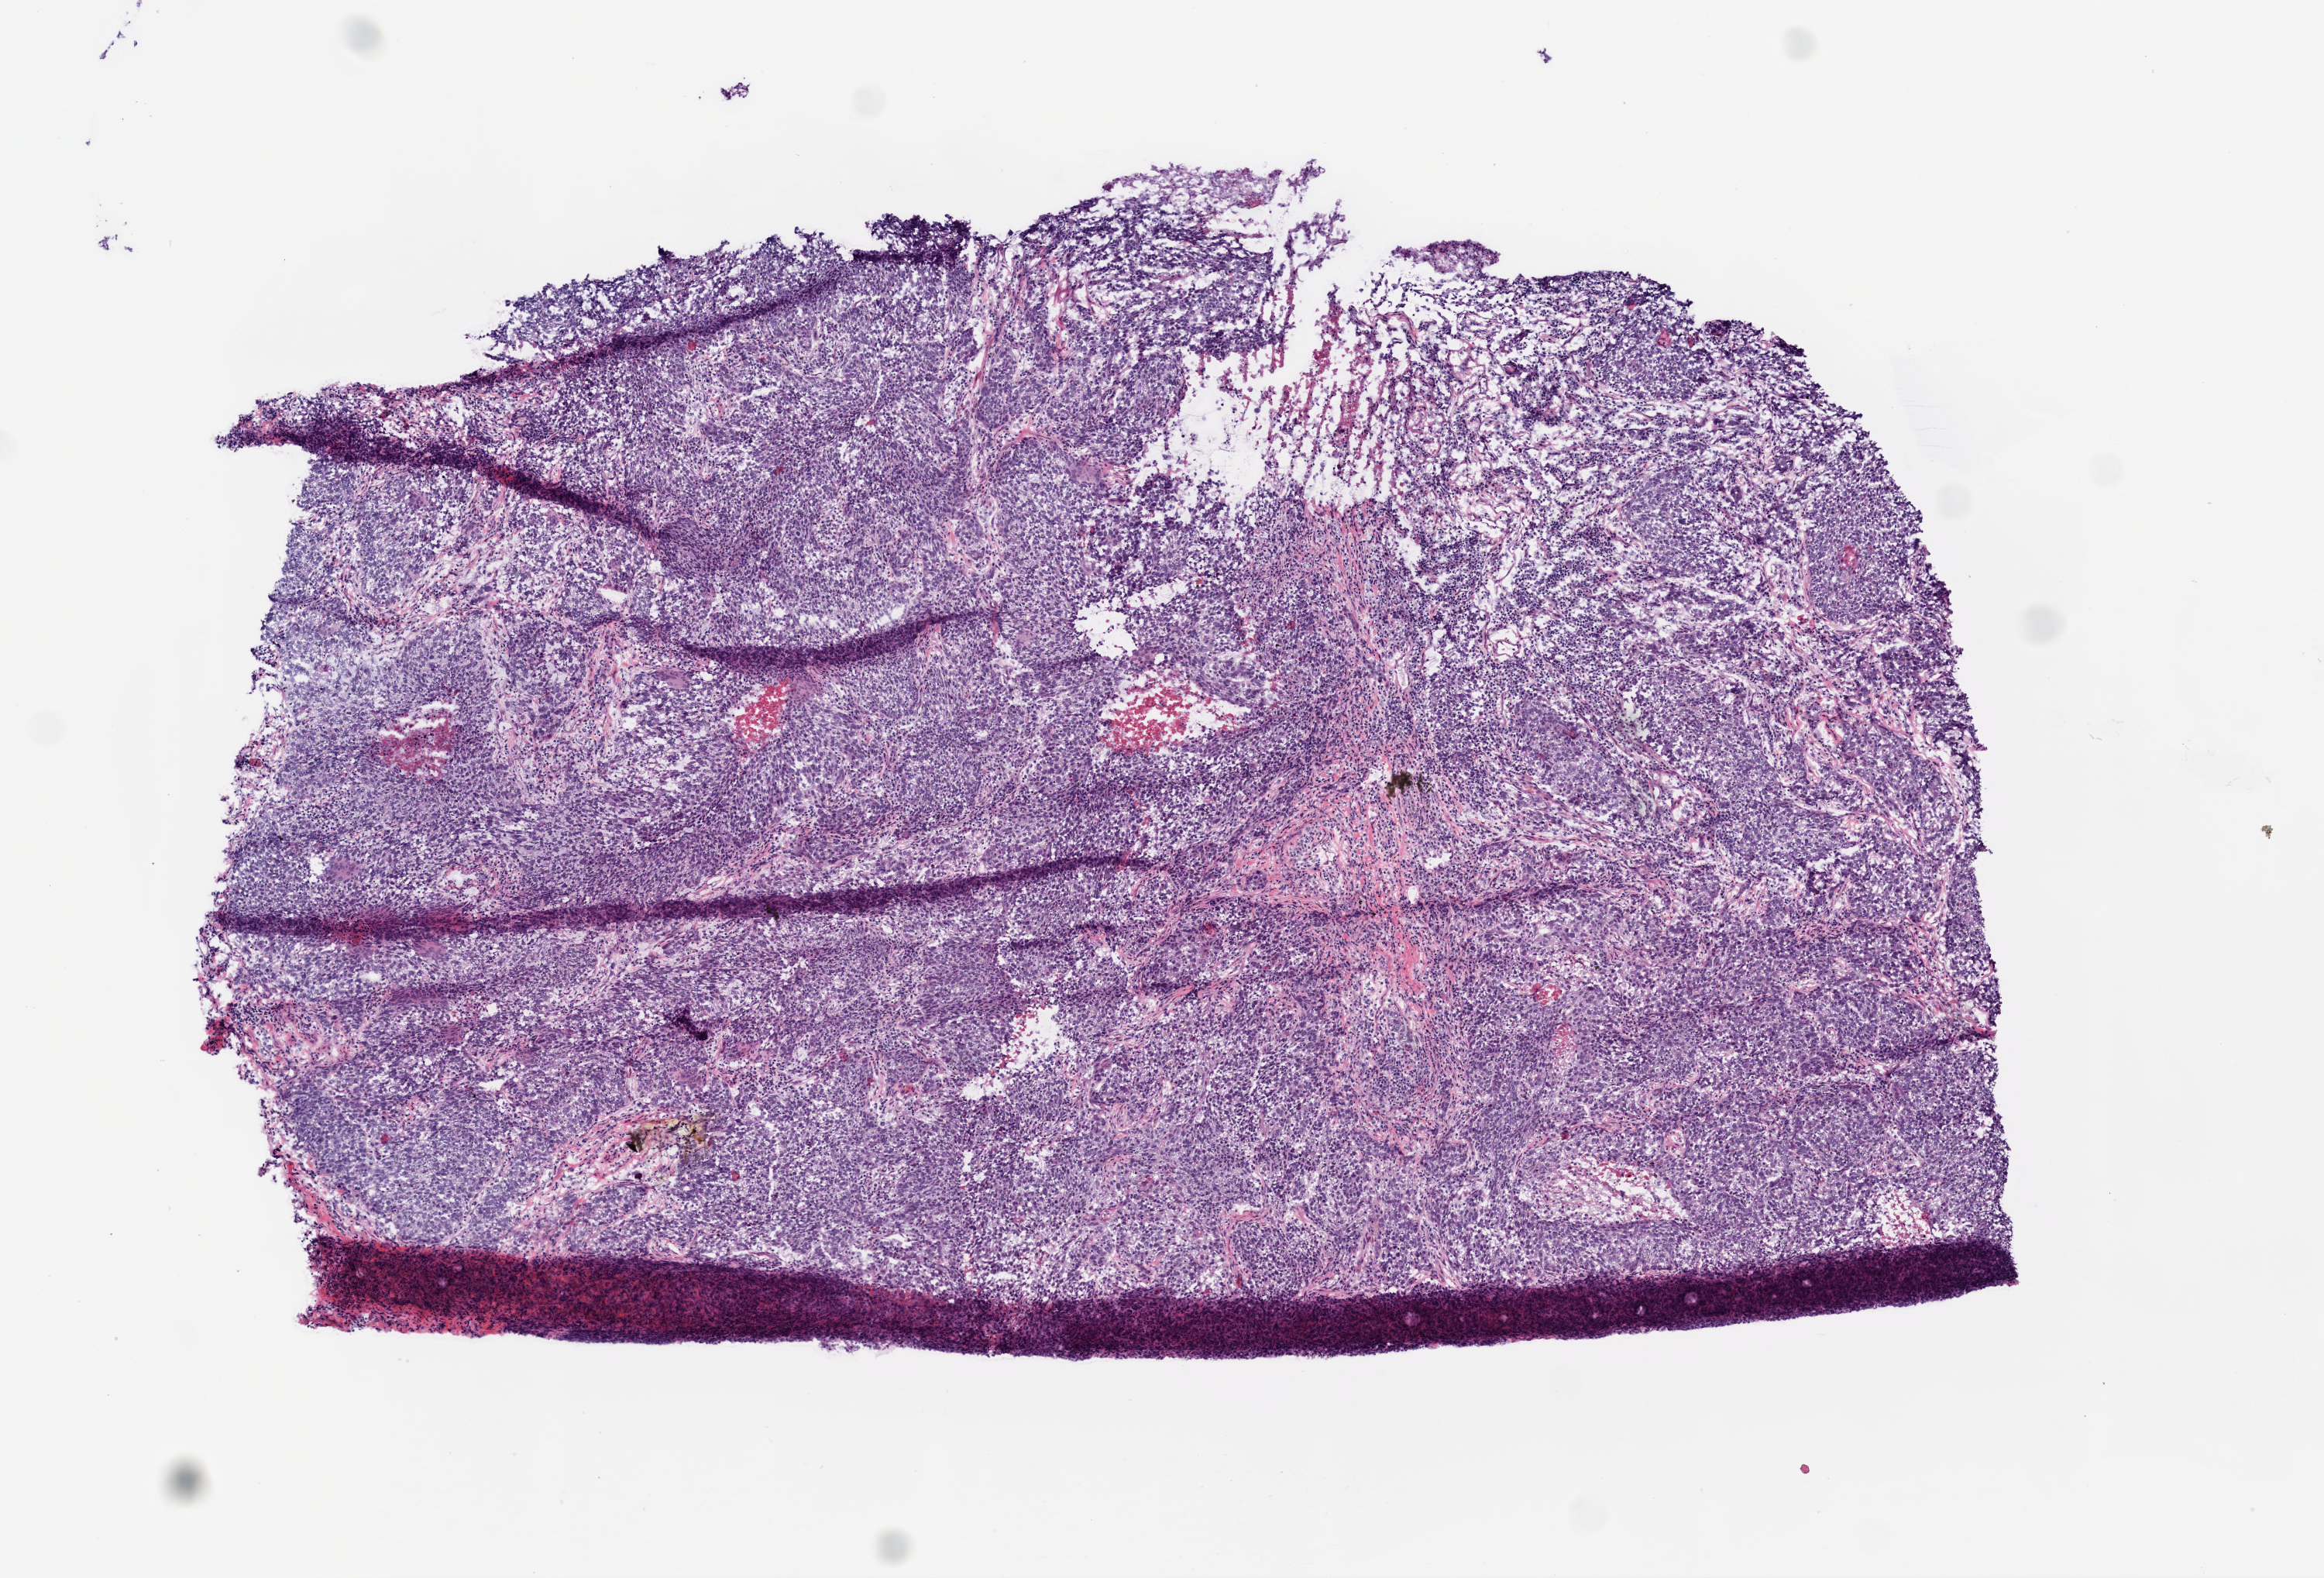
Digitized H&E-stained tissue section (whole slide), low-resolution overview of the scanned area, about 6.0 x 4.1 mm (slide scanned at 20x). Frozen section. Primary tumour sample from the lung. Patient: male, age at initial diagnosis 81 years. Composition of this section per pathologist review: tumour cells 85%, tumour nuclei 80%, normal cells 0%, stromal cells 10%, necrosis 5%. Infiltration values recorded for this section: lymphocyte infiltration 10%.
AJCC pathologic stage: IIB. Pathologic diagnosis: Squamous cell carcinoma, NOS (lower lobe, lung). Laterality: right.